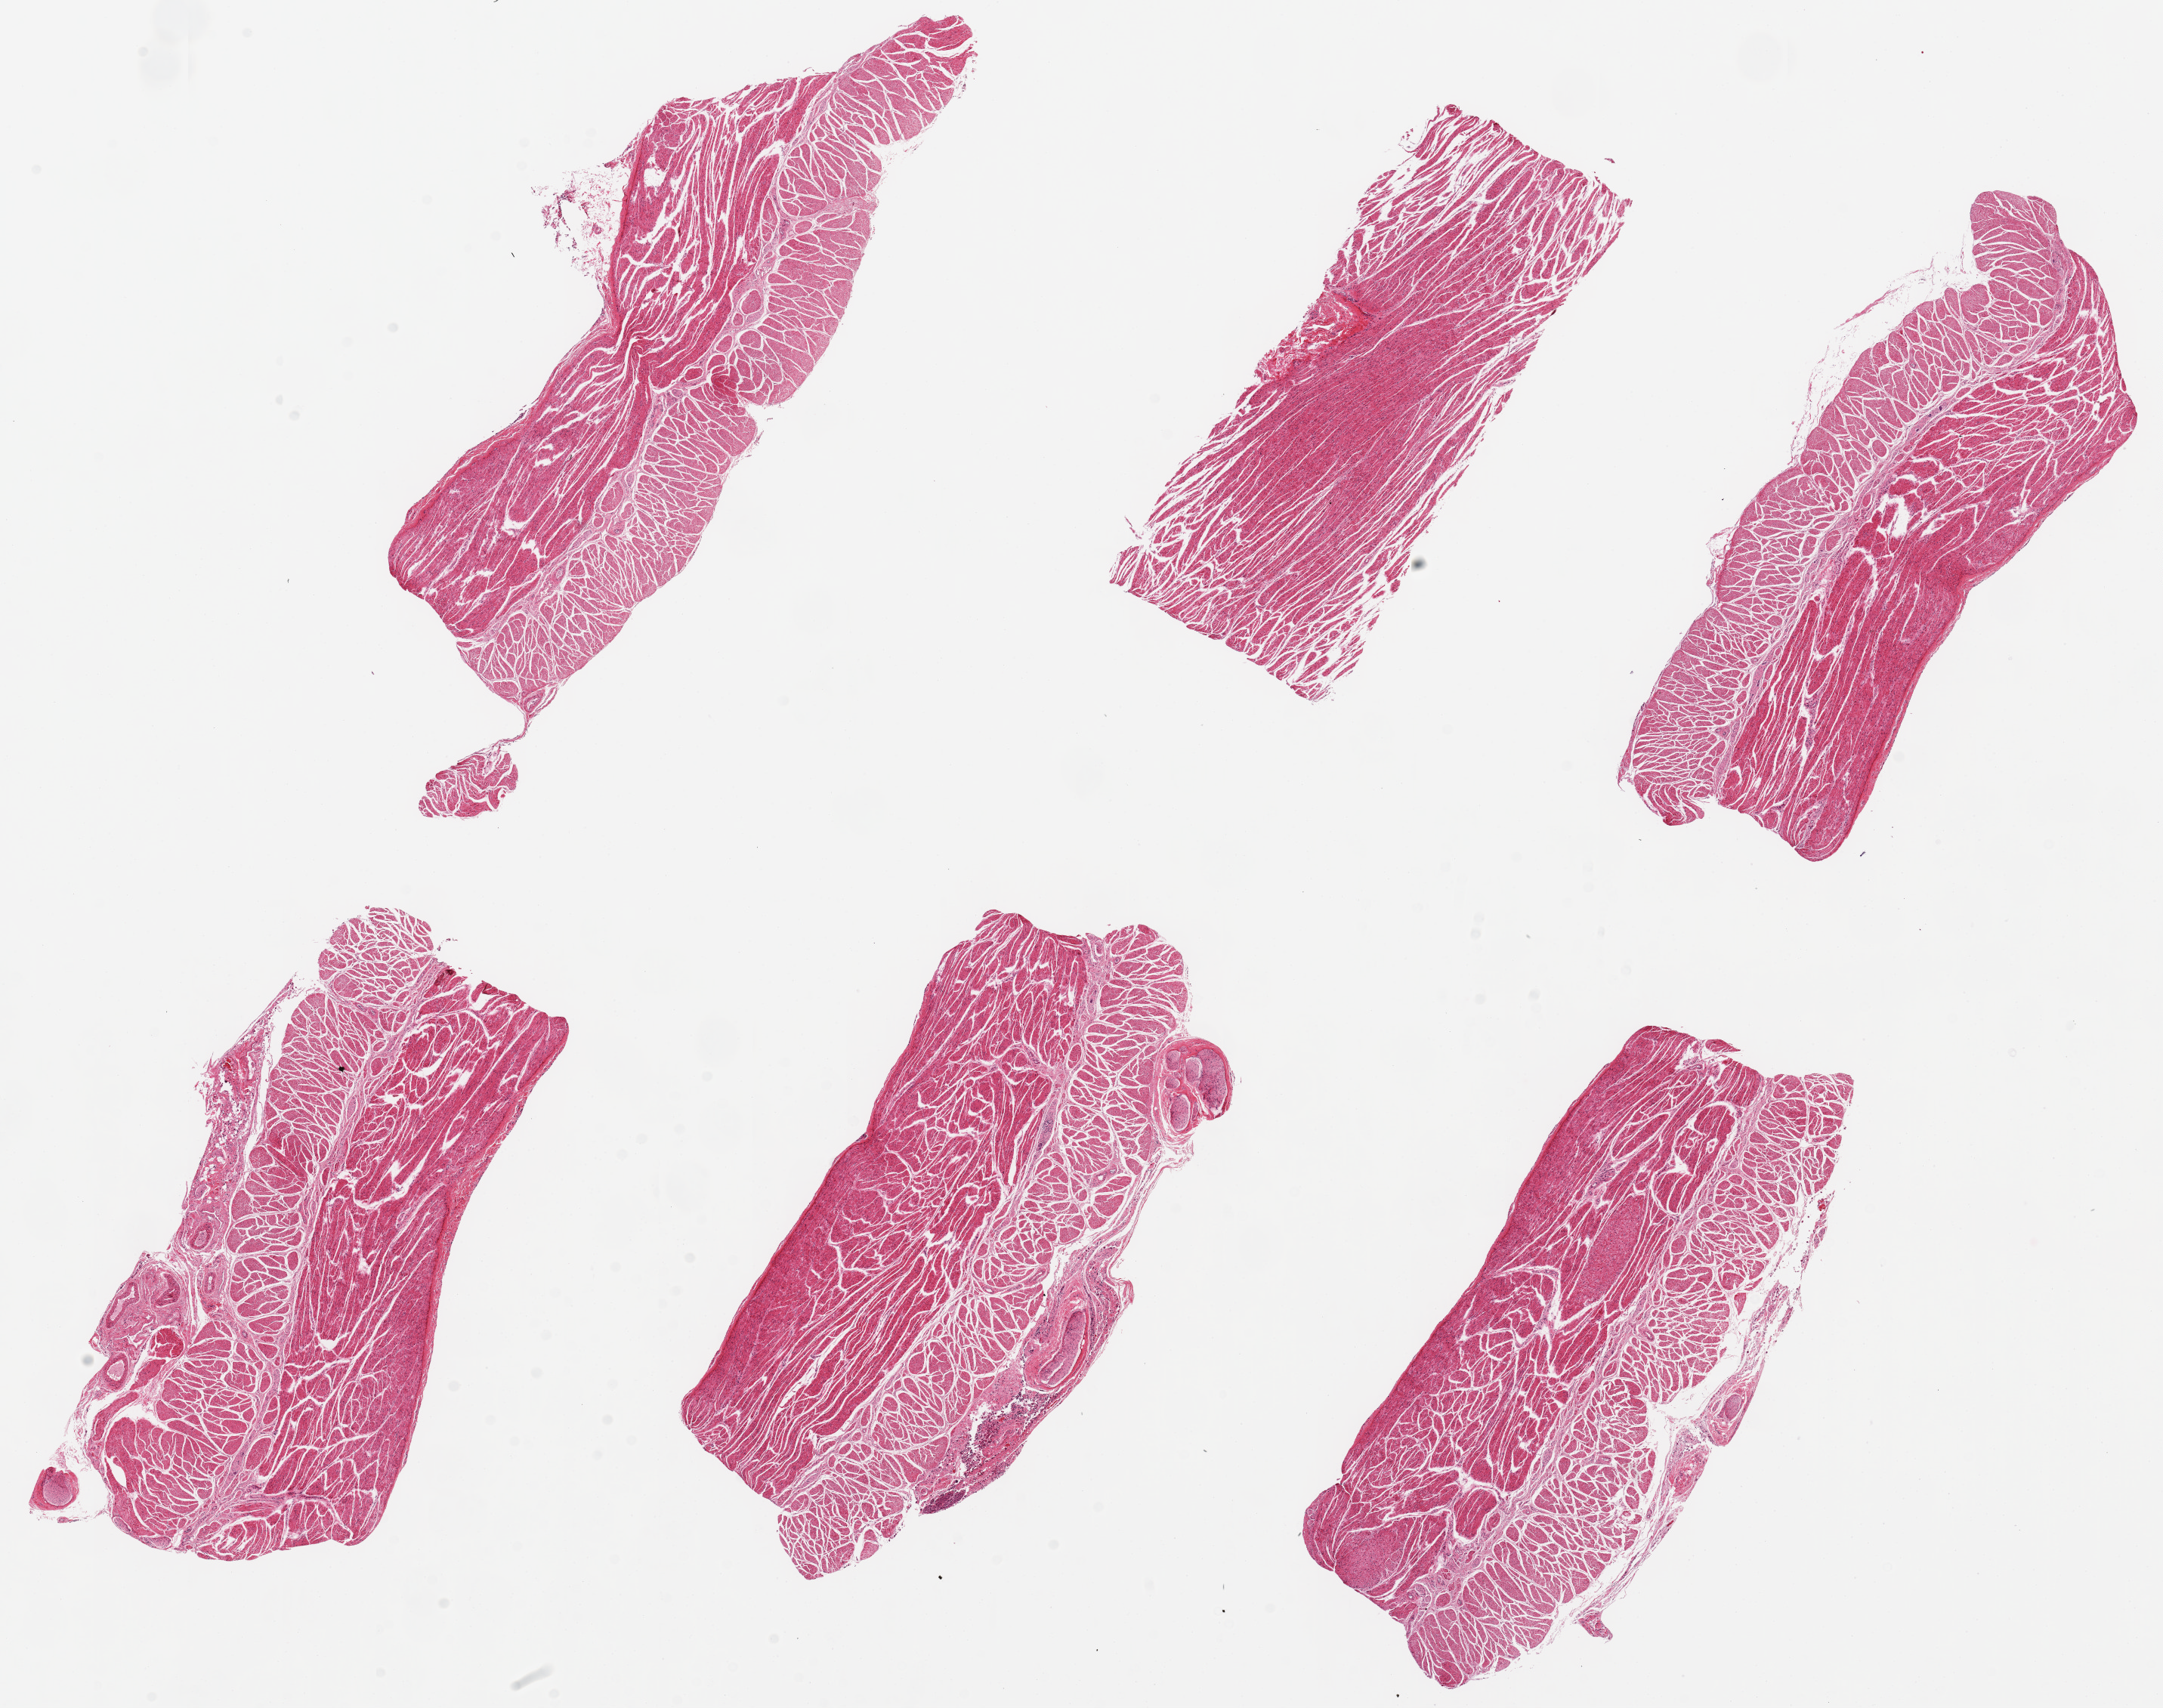
Whole-slide image, hematoxylin and eosin (H&E) stain, brightfield, shown as a low-resolution overview of the whole scanned area (about 22.6 x 17.9 mm, acquisition: 20x scan); PAXgene-fixed, paraffin-embedded tissue; sampled site (target tissue): gastroesophageal junction; donor tissue sample. Donor: female.
• pathologist's review note for this sample: 6 pieces. up to 10x4mm; well trimmed, all muscularis propria